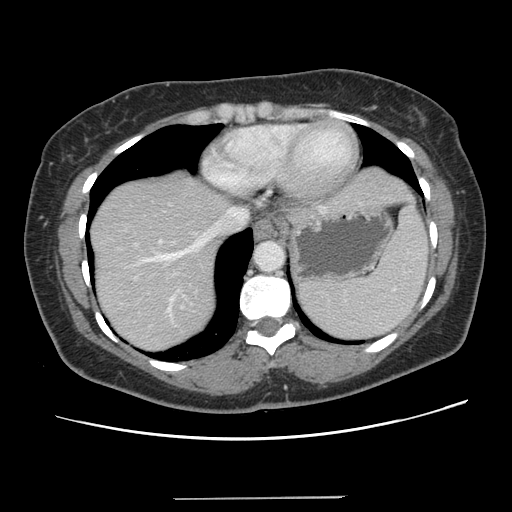
Contrast-enhanced abdominal CT, one axial slice; position 115 of 141 along the scan axis; intravenous contrast given; soft-tissue window (W 400 / L 40 HU); 512 × 512 image matrix, field of view 366 × 366 mm. Female patient, age 53 years. Case-level facts recorded for this patient, not image findings: diagnosis: colorectal cancer liver metastases, imaged before liver resection; multiple liver metastases: no; largest metastasis: 14.5 cm; disease in both lobes: yes.
Annotated regions visible in this slice (expert manual segmentation):
- hepatic veins: bounding box (x1, y1, x2, y2) in pixels: (113, 207, 248, 303)
- liver: (90, 167, 410, 352)
- planned liver remnant (the part of the liver to remain after resection): (90, 211, 224, 352)
- portal vein (with intrahepatic branches): (135, 239, 183, 308)